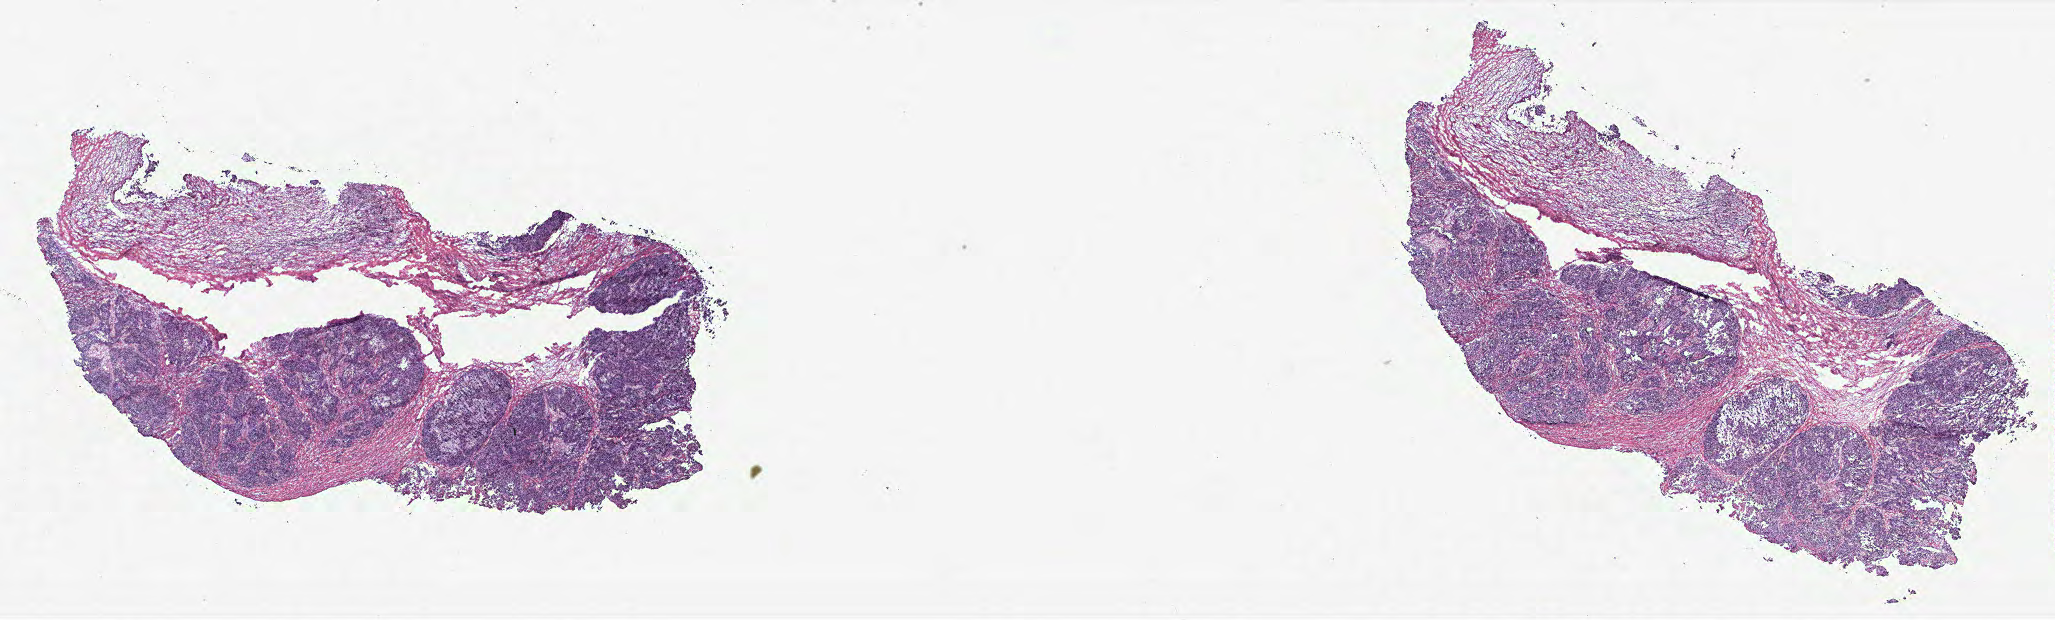
Digitized Hematoxylin and eosin (H&E) stained tissue section (whole slide) — a low-resolution overview of the entire scanned area, about 32.9 x 9.9 mm (from a 40x scan), ovary, tissue type not recorded.
Patient diagnosis (cohort enrolment): ovarian cancer (ovary).